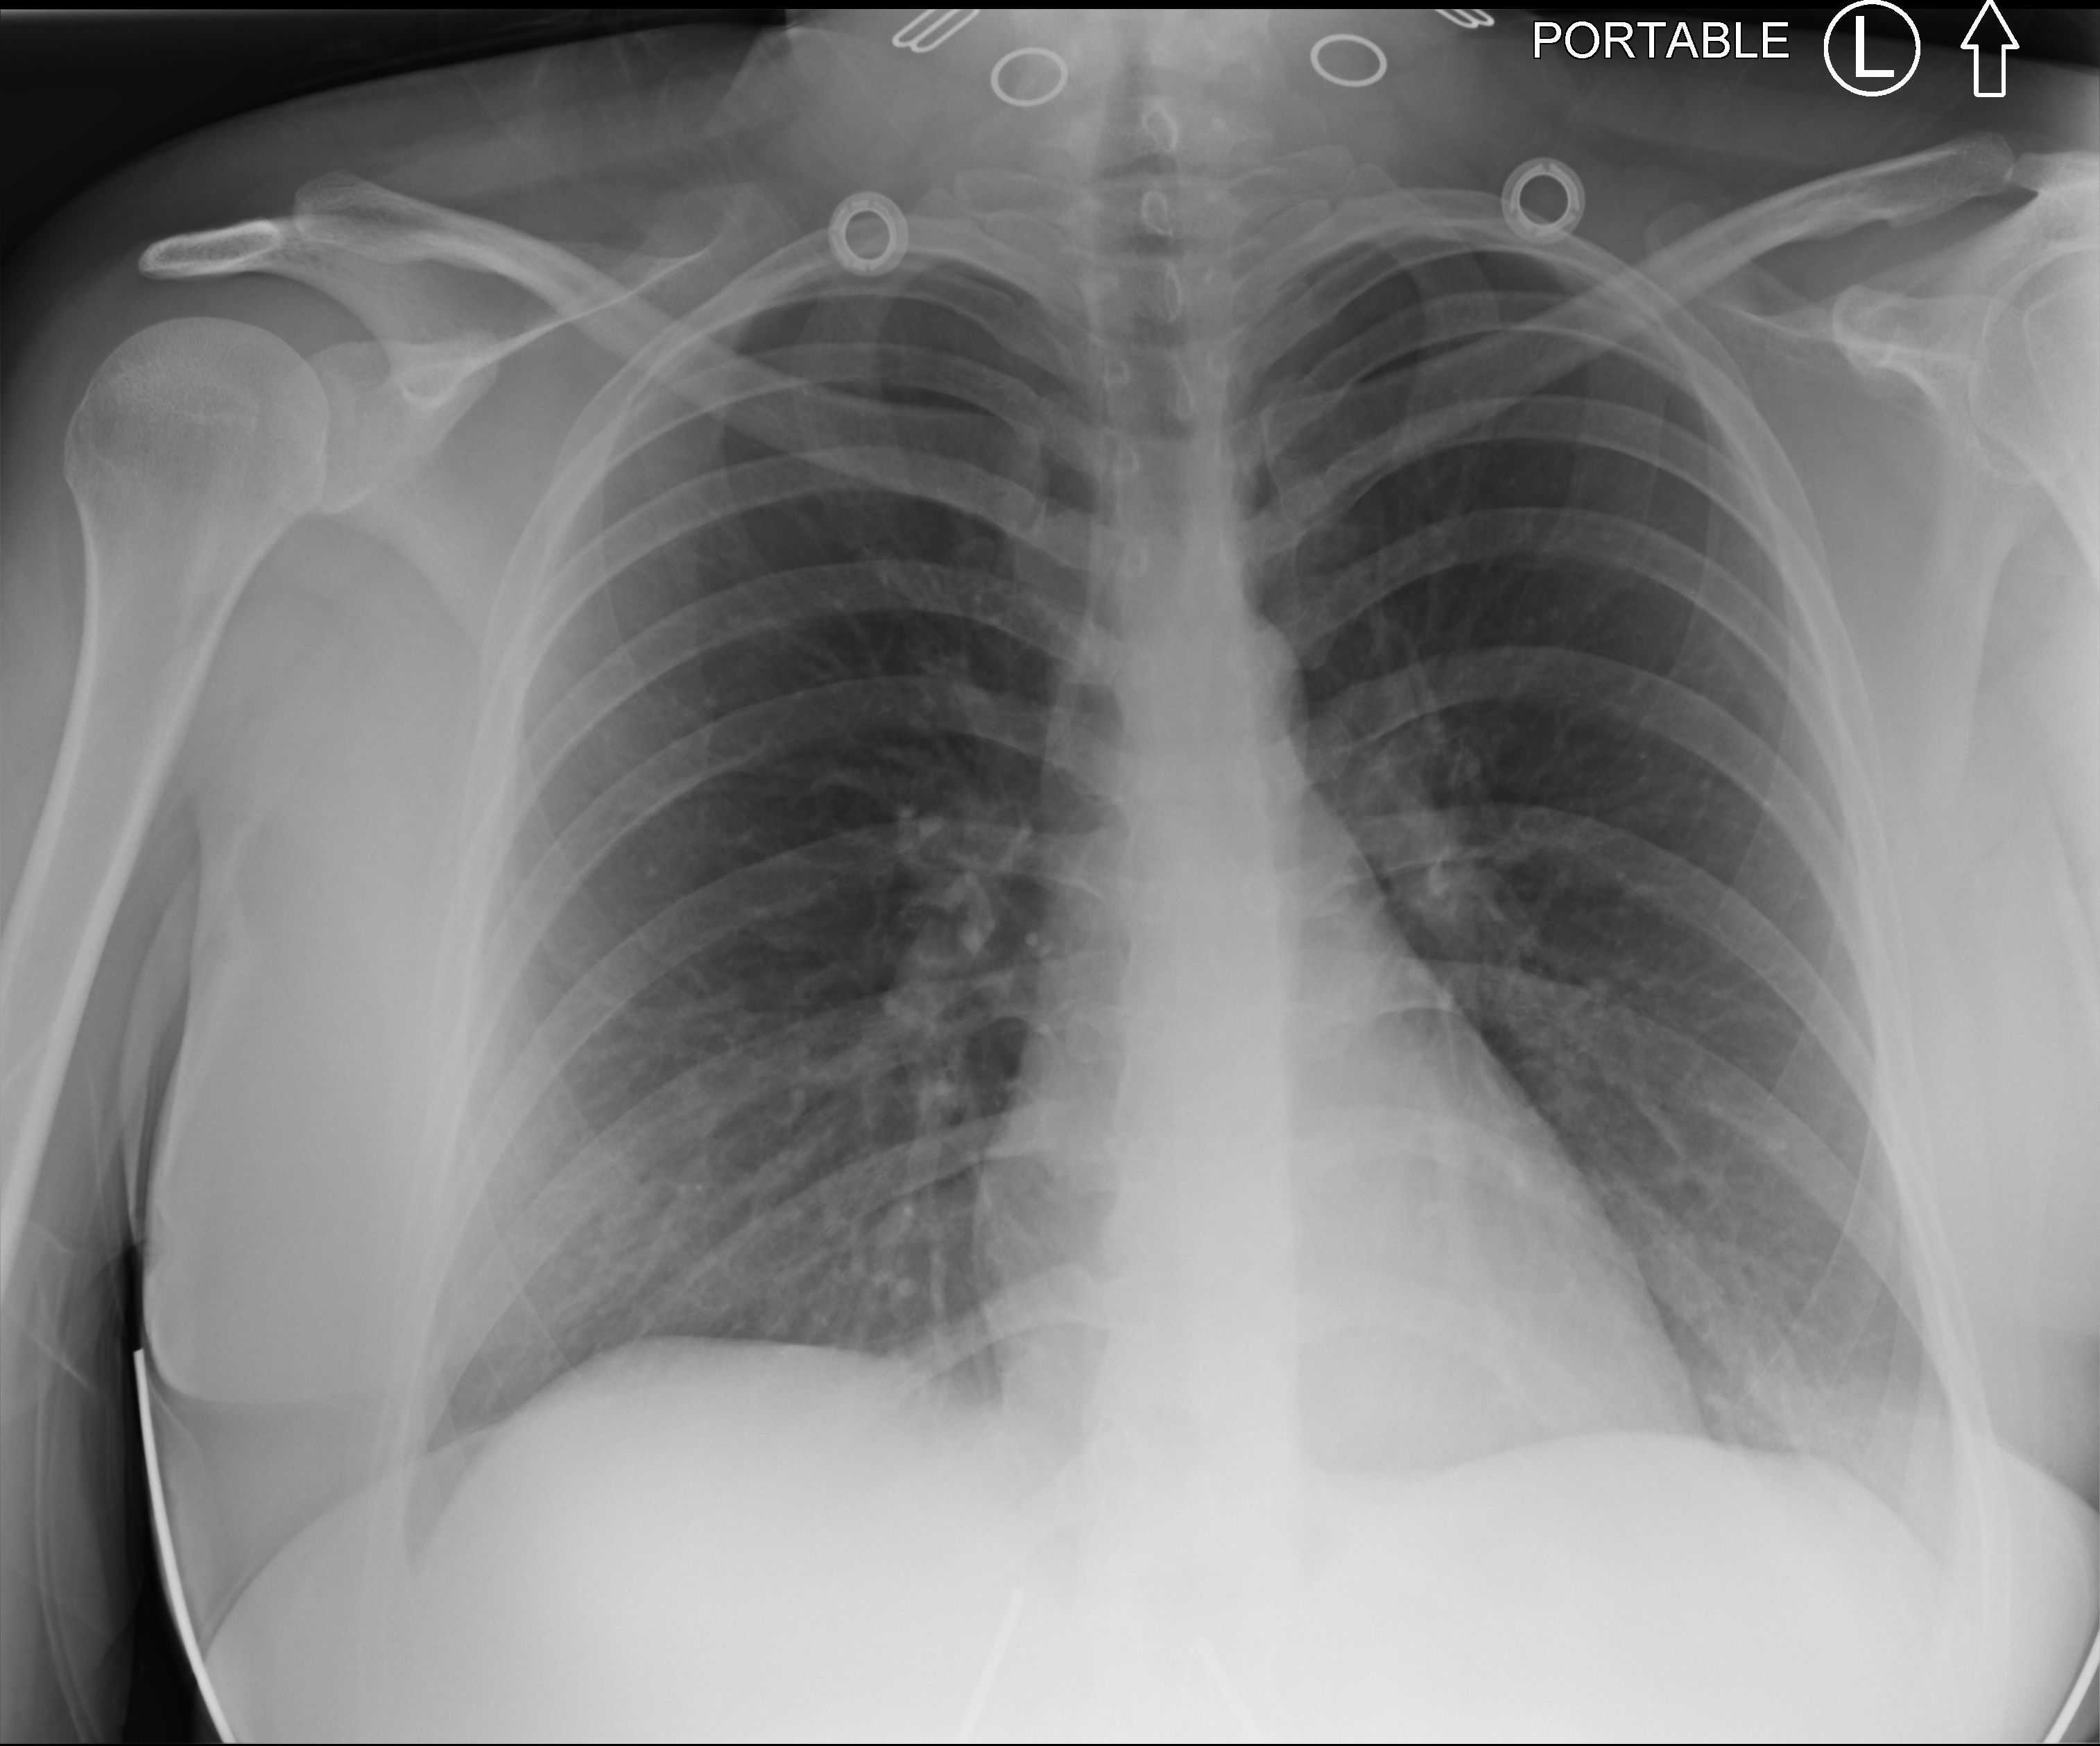
Bedside chest radiograph (computed radiography); anteroposterior (AP) projection. Patient hospitalised with COVID-19; female, aged 18–59 years.
Admission-level facts for this patient (not findings on this image; timing relative to this image not recorded): admitted to intensive care during this hospital stay: no; mechanically ventilated during this hospital stay: no; length of hospital stay: 1 day.